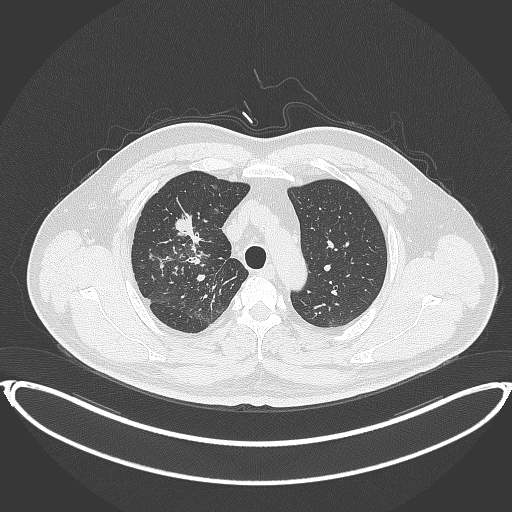
Chest CT, one axial slice; position 298 of 399 along the scan axis; reconstruction kernel B70f; lung window (W 1500 / L -600 HU); 512 × 512 image matrix, field of view 445 × 445 mm. Male patient, age 53 years. From the clinical record (not read from this slice): clinical TNM (as recorded): T2a N0 M0.
Annotated regions visible in this slice (bounding box drawn by a radiologist):
- lung tumour (recorded histology: adenocarcinoma): bounding box <170,211,201,246> (left, top, right, bottom; pixels)